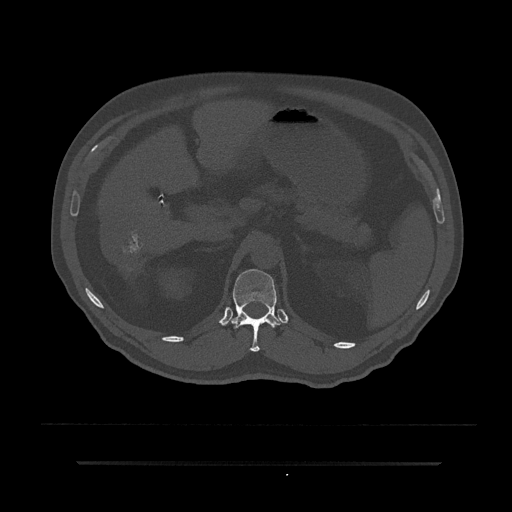
CT including the spine, one axial slice; slice 211 of 797 in the series (ordered by position); 120 kVp; bone window (W 1800 / L 400 HU); 0.5 mm slice thickness; 512 × 512 image matrix, field of view 464 × 464 mm. Male patient, age 59 years. From the clinical record (not read from this slice): primary cancer: bile ducts; vertebrae with lytic lesions (as recorded): T10.
Annotated regions visible in this slice (semi-automatically segmented with operator editing):
- T12 vertebra: bounding box (x1, y1, x2, y2) in pixels: (231, 269, 282, 352)